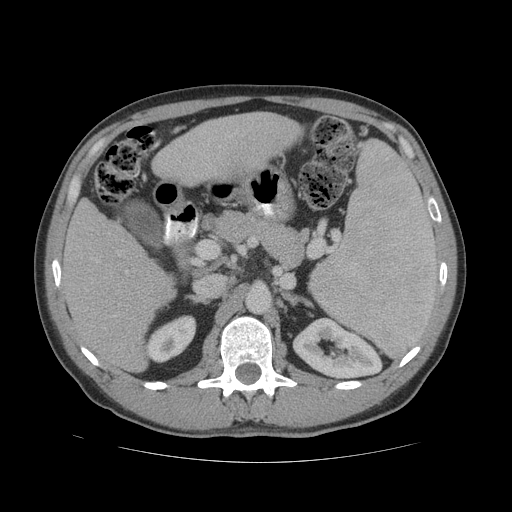
Contrast-enhanced abdominal CT (liver protocol), one axial slice. Slice 29 of 81 in the series (ordered by position). Reconstruction kernel STANDARD. 140 kVp. Soft-tissue window (W 400 / L 40 HU). 2.5 mm slice thickness. 512 × 512 image matrix, field of view 400 × 400 mm. Case-level facts recorded for this patient, not image findings: diagnosis: hepatocellular carcinoma (patient treated with transarterial chemoembolisation; whether this scan precedes or follows treatment is not stated here); TNM stage (as recorded): Stage-IVB; Child-Pugh class: B.
Structures marked on this image (semi-automatically segmented with operator editing):
- liver parenchyma outside the tumour (the mass and vessels are separate outlines, so this box may not span the whole liver): bounding box <60,112,300,372> (left, top, right, bottom; pixels)